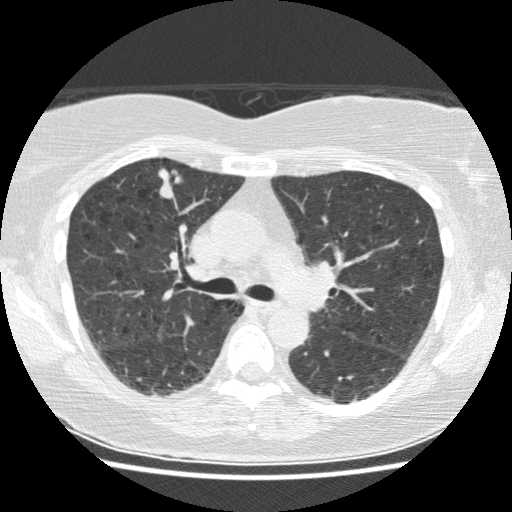
Low-dose screening chest CT, axial slice. Baseline annual screen. Lung window (W 1500 / L -600 HU). Standard (soft-tissue) reconstruction kernel (STANDARD). Female, age 63 years at enrolment. Current smoker at enrolment.
Expert reader's lesion annotation, bounding box [x1, y1, x2, y2] px = [144, 157, 186, 209]. Reader record for this screening exam (exam-level; its link to the box is not recorded): non-calcified nodule or mass ≥4 mm, right upper lobe, 18 × 14 mm, spiculated (stellate) margins, soft tissue attenuation.